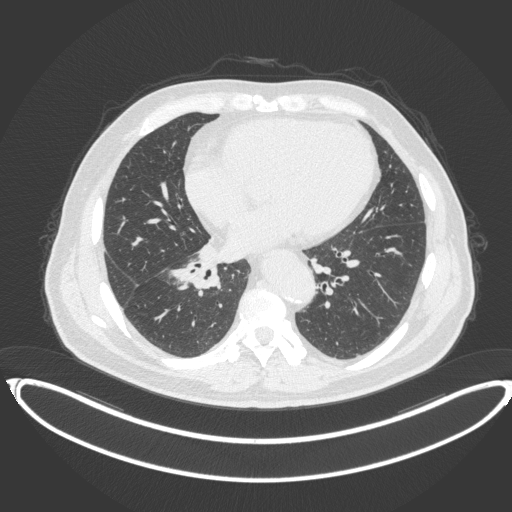
Chest CT, one axial slice. Position 168 of 383 along the scan axis. Reconstruction kernel B31f. 120 kVp. Lung window (W 1500 / L -600 HU). 1 mm slice thickness. 512 × 512 image matrix, field of view 448 × 448 mm. Male patient, age 61 years. From the clinical record (not read from this slice): clinical TNM (as recorded): T1b N1 M0.
Structures marked on this image (rectangle marked by the reading radiologist):
- lung tumour (recorded histology: squamous cell carcinoma): box from (x=181, y=258) to (x=220, y=287) px